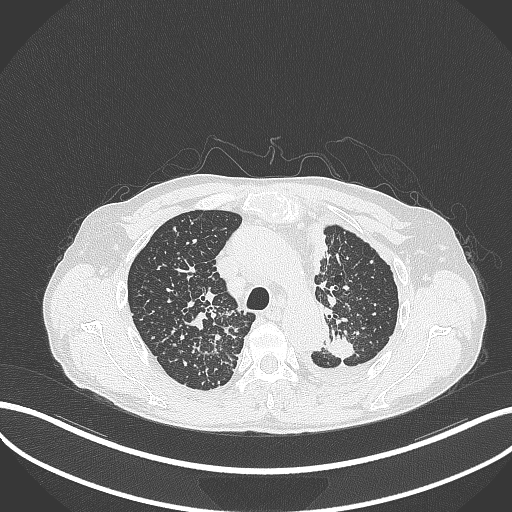
Chest CT, one axial slice; slice 260 of 325 in the series (ordered by position); reconstruction kernel B70f; 120 kVp; lung window (W 1500 / L -600 HU); 1 mm slice thickness; 512 × 512 image matrix, field of view 400 × 400 mm. Male patient, age 58 years. Case-level facts recorded for this patient, not image findings: clinical TNM (as recorded): T1c N3 M1.
Annotated regions visible in this slice (bounding box drawn by a radiologist):
- lung tumour (recorded histology: adenocarcinoma): bounding box (x1, y1, x2, y2) in pixels: (321, 332, 358, 363)